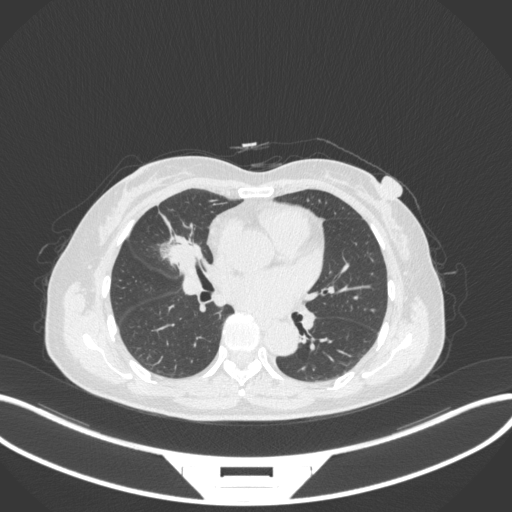
Chest CT, one axial slice; slice 153 of 282 in the series (ordered by position); lung window (W 1500 / L -600 HU); 1 mm slice thickness; 512 × 512 image matrix, field of view 400 × 400 mm. Female patient, age 51 years. From the clinical record (not read from this slice): clinical TNM (as recorded): T1c N0 M0; histopathological grade: G2.
Structures marked on this image (bounding box drawn by a radiologist):
- lung tumour (recorded histology: adenocarcinoma): box from (x=154, y=228) to (x=207, y=276) px